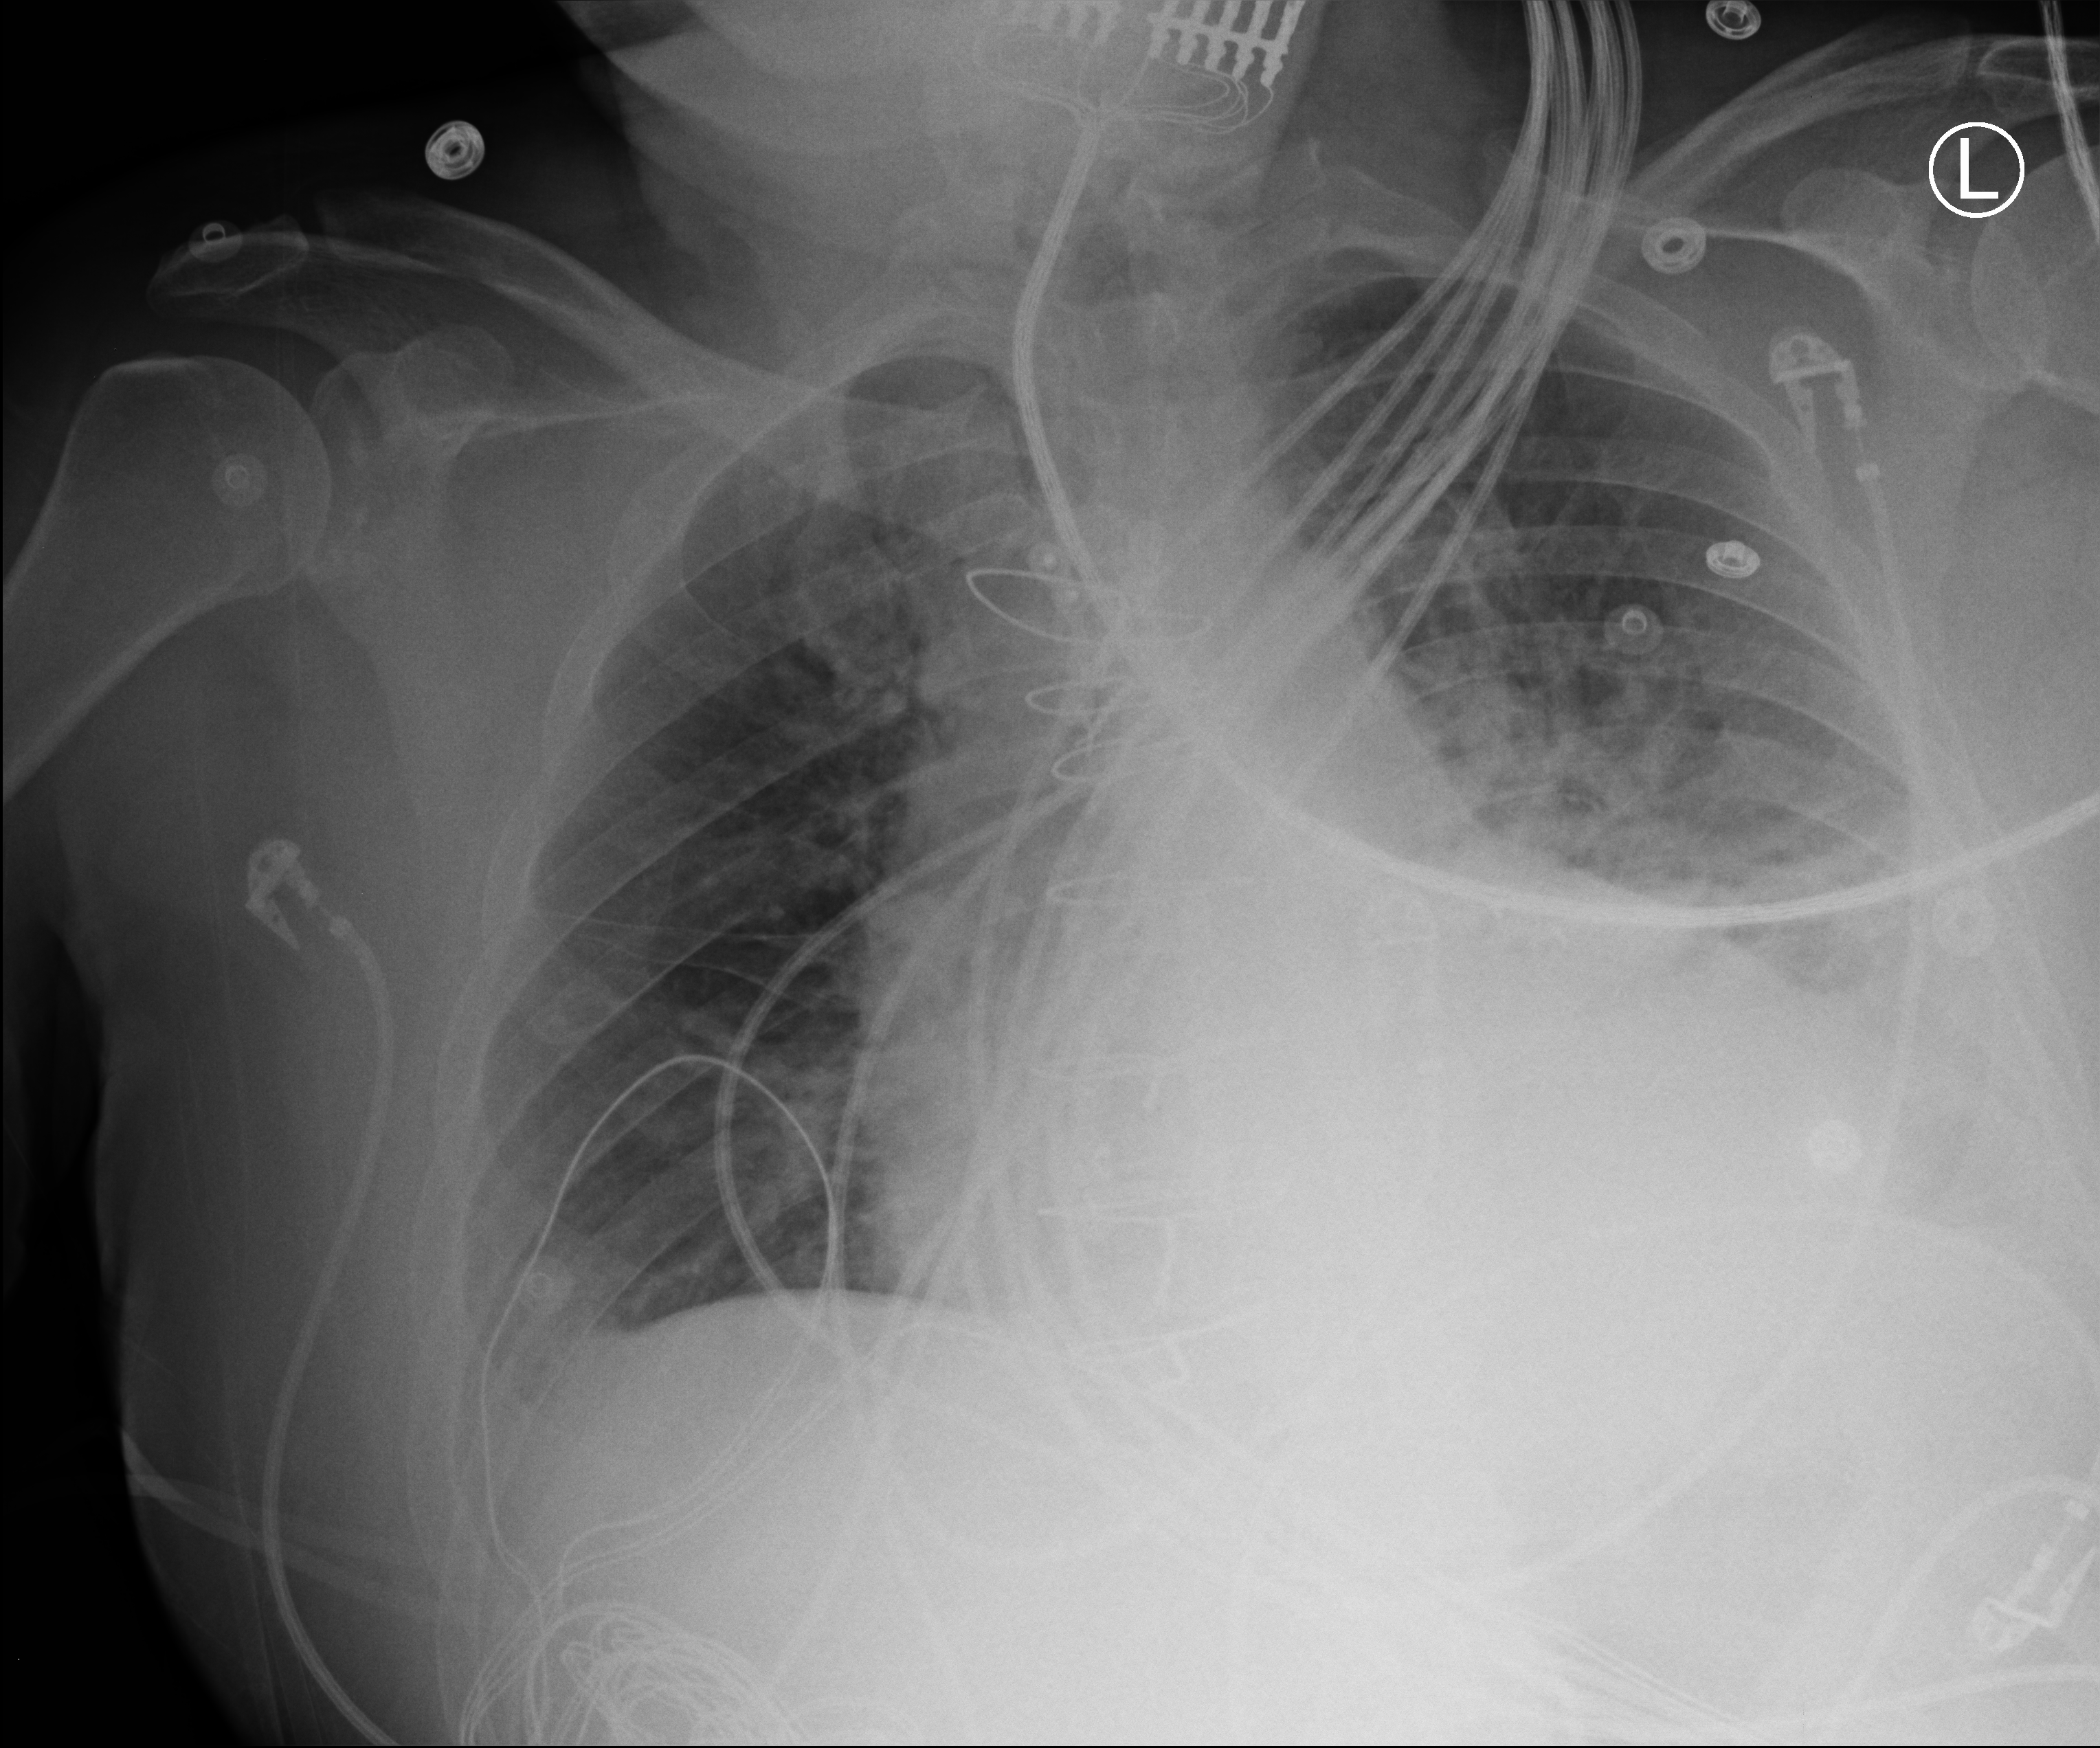
Portable chest radiograph. Patient hospitalised with COVID-19; male, aged 18–59 years.
Hospital-stay facts (about this admission, not read from this image; timing relative to this image not recorded): mechanically ventilated during this hospital stay: no; admitted to intensive care during this hospital stay: no.